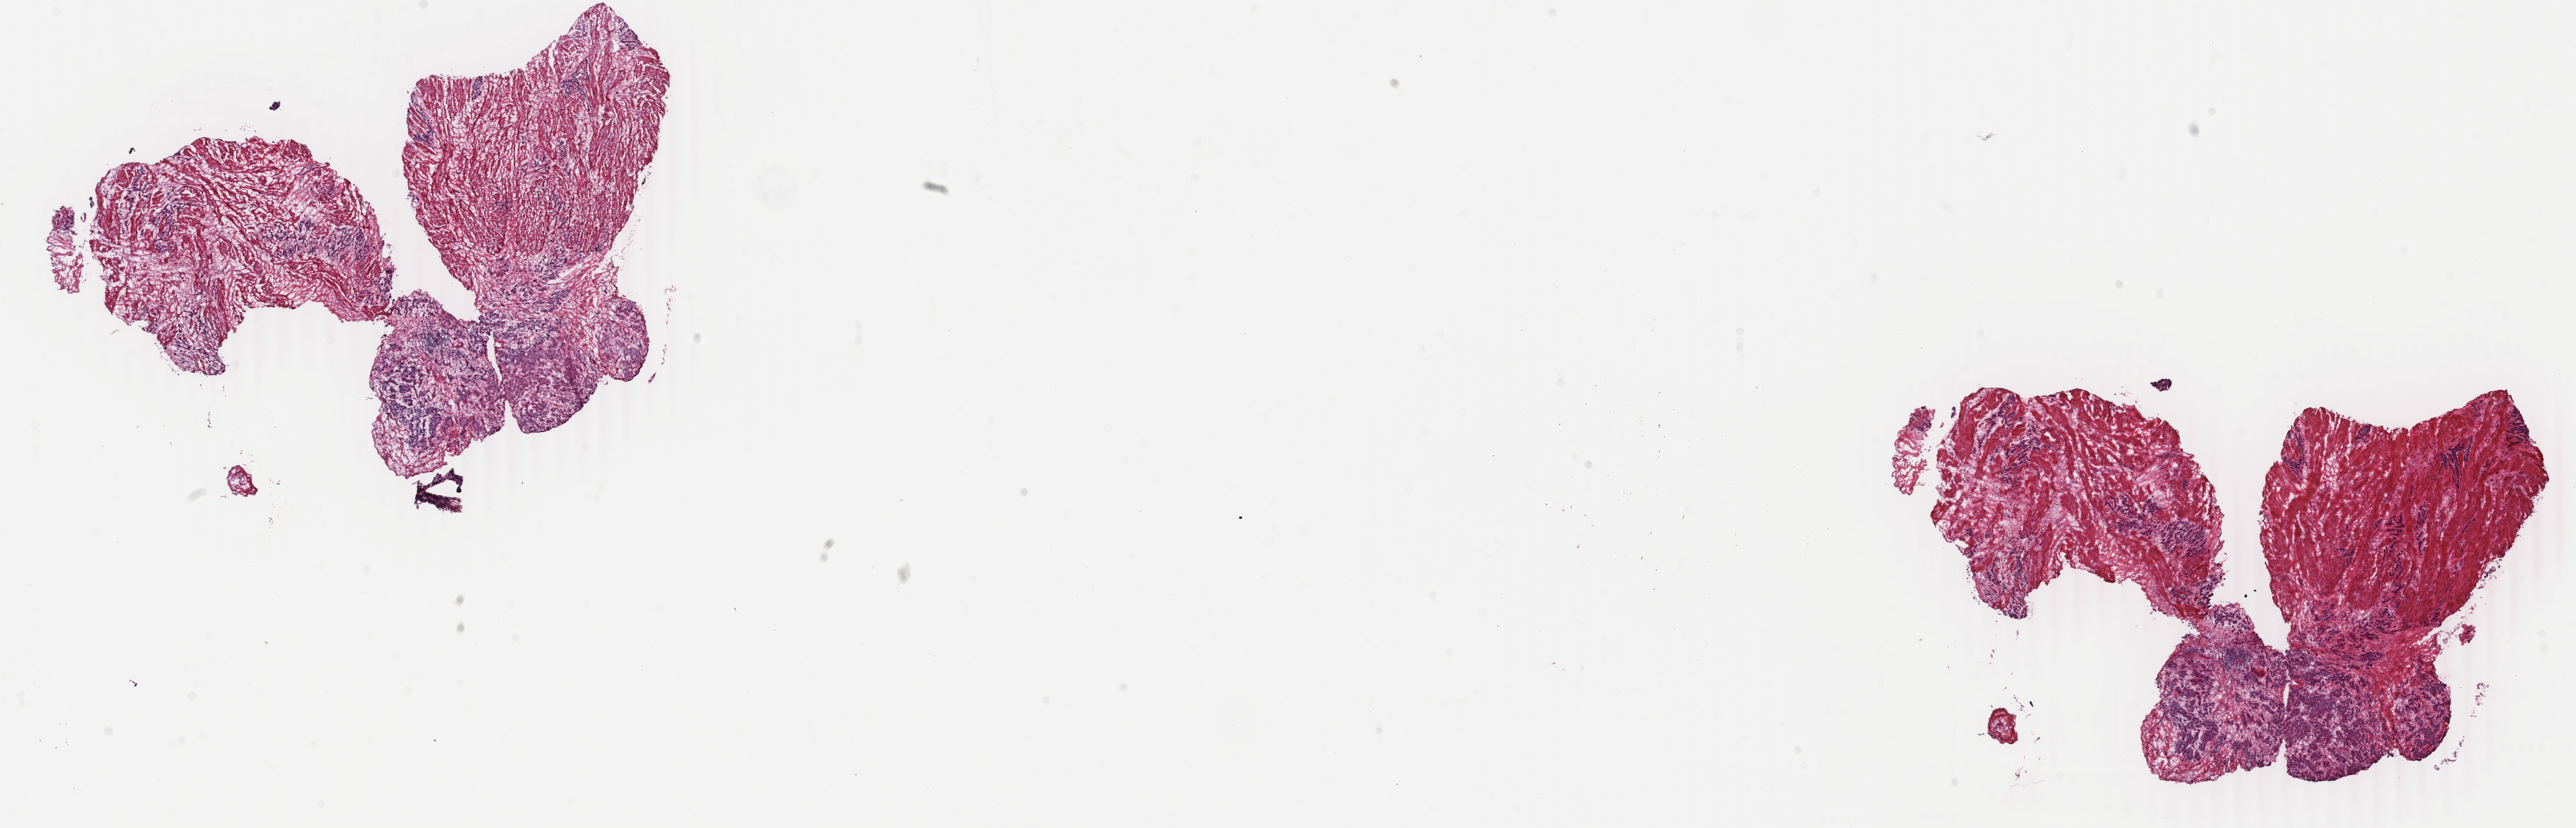
Digitized H&E-stained tissue section (whole slide), whole scanned area (about 26.7 x 8.6 mm) shown as a low-resolution overview; frozen section; bladder, primary tumour sample. Patient: male, age at initial diagnosis 84 years. Histologic grade: high grade. Pathologist review of this section (percent, as recorded): tumour cells 55%, tumour nuclei 55%, normal cells 0%, stromal cells 45%, necrosis 0%. Infiltration values recorded for this section: lymphocyte infiltration 3%, monocyte infiltration 1%, neutrophil infiltration 1%.
Lymph nodes positive (case pathology): 8 of 13 examined. AJCC pathologic stage: IV. Diagnosis: Papillary transitional cell carcinoma.